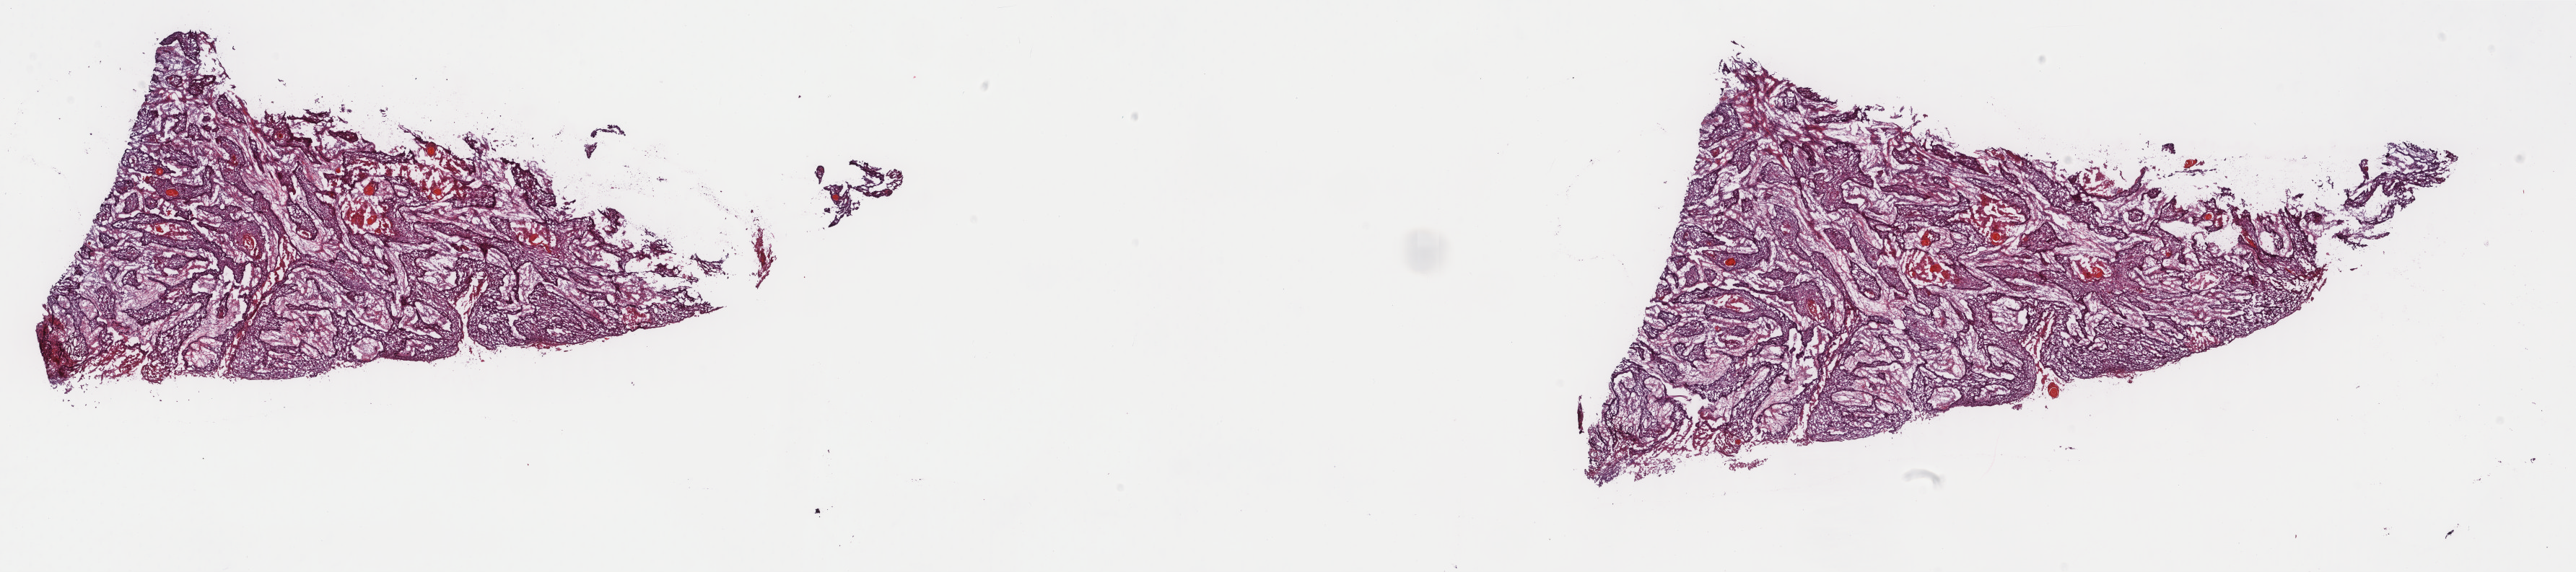
Whole-slide histology image, H&E-stained — a low-resolution overview of the entire scanned area, about 28.3 x 6.3 mm (acquisition: 40x scan), frozen section from the top of the tissue portion, sample: primary tumour, esophagus. Patient: male, age at initial diagnosis 62 years. Histologic grade: G1 (well differentiated). Slide review estimates, as recorded: tumour cells 95%, tumour nuclei 85%, normal cells 0%, stromal cells 0%, necrosis 5%. Infiltration values recorded for this section: lymphocyte infiltration 0%, monocyte infiltration 0%, neutrophil infiltration 0%.
- pathologic diagnosis: Squamous cell carcinoma, NOS
- AJCC pathologic stage: IIA
- TNM: T3 N0 M0